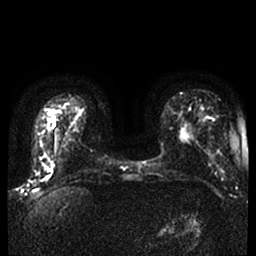
Breast MRI, one axial slice. Slice 11 of 42 in the series (ordered by position). Diffusion-weighted series; image 2 of 4 stored at this slice position (different b-values; order by instance number). 1.5 T. 4 mm slice thickness. 256 × 256 image matrix, field of view 340 × 340 mm. Female patient.
Structures marked on this image (expert manual segmentation):
- tumour on diffusion-weighted imaging: bounding box [x1, y1, x2, y2] px = [43, 175, 50, 181]